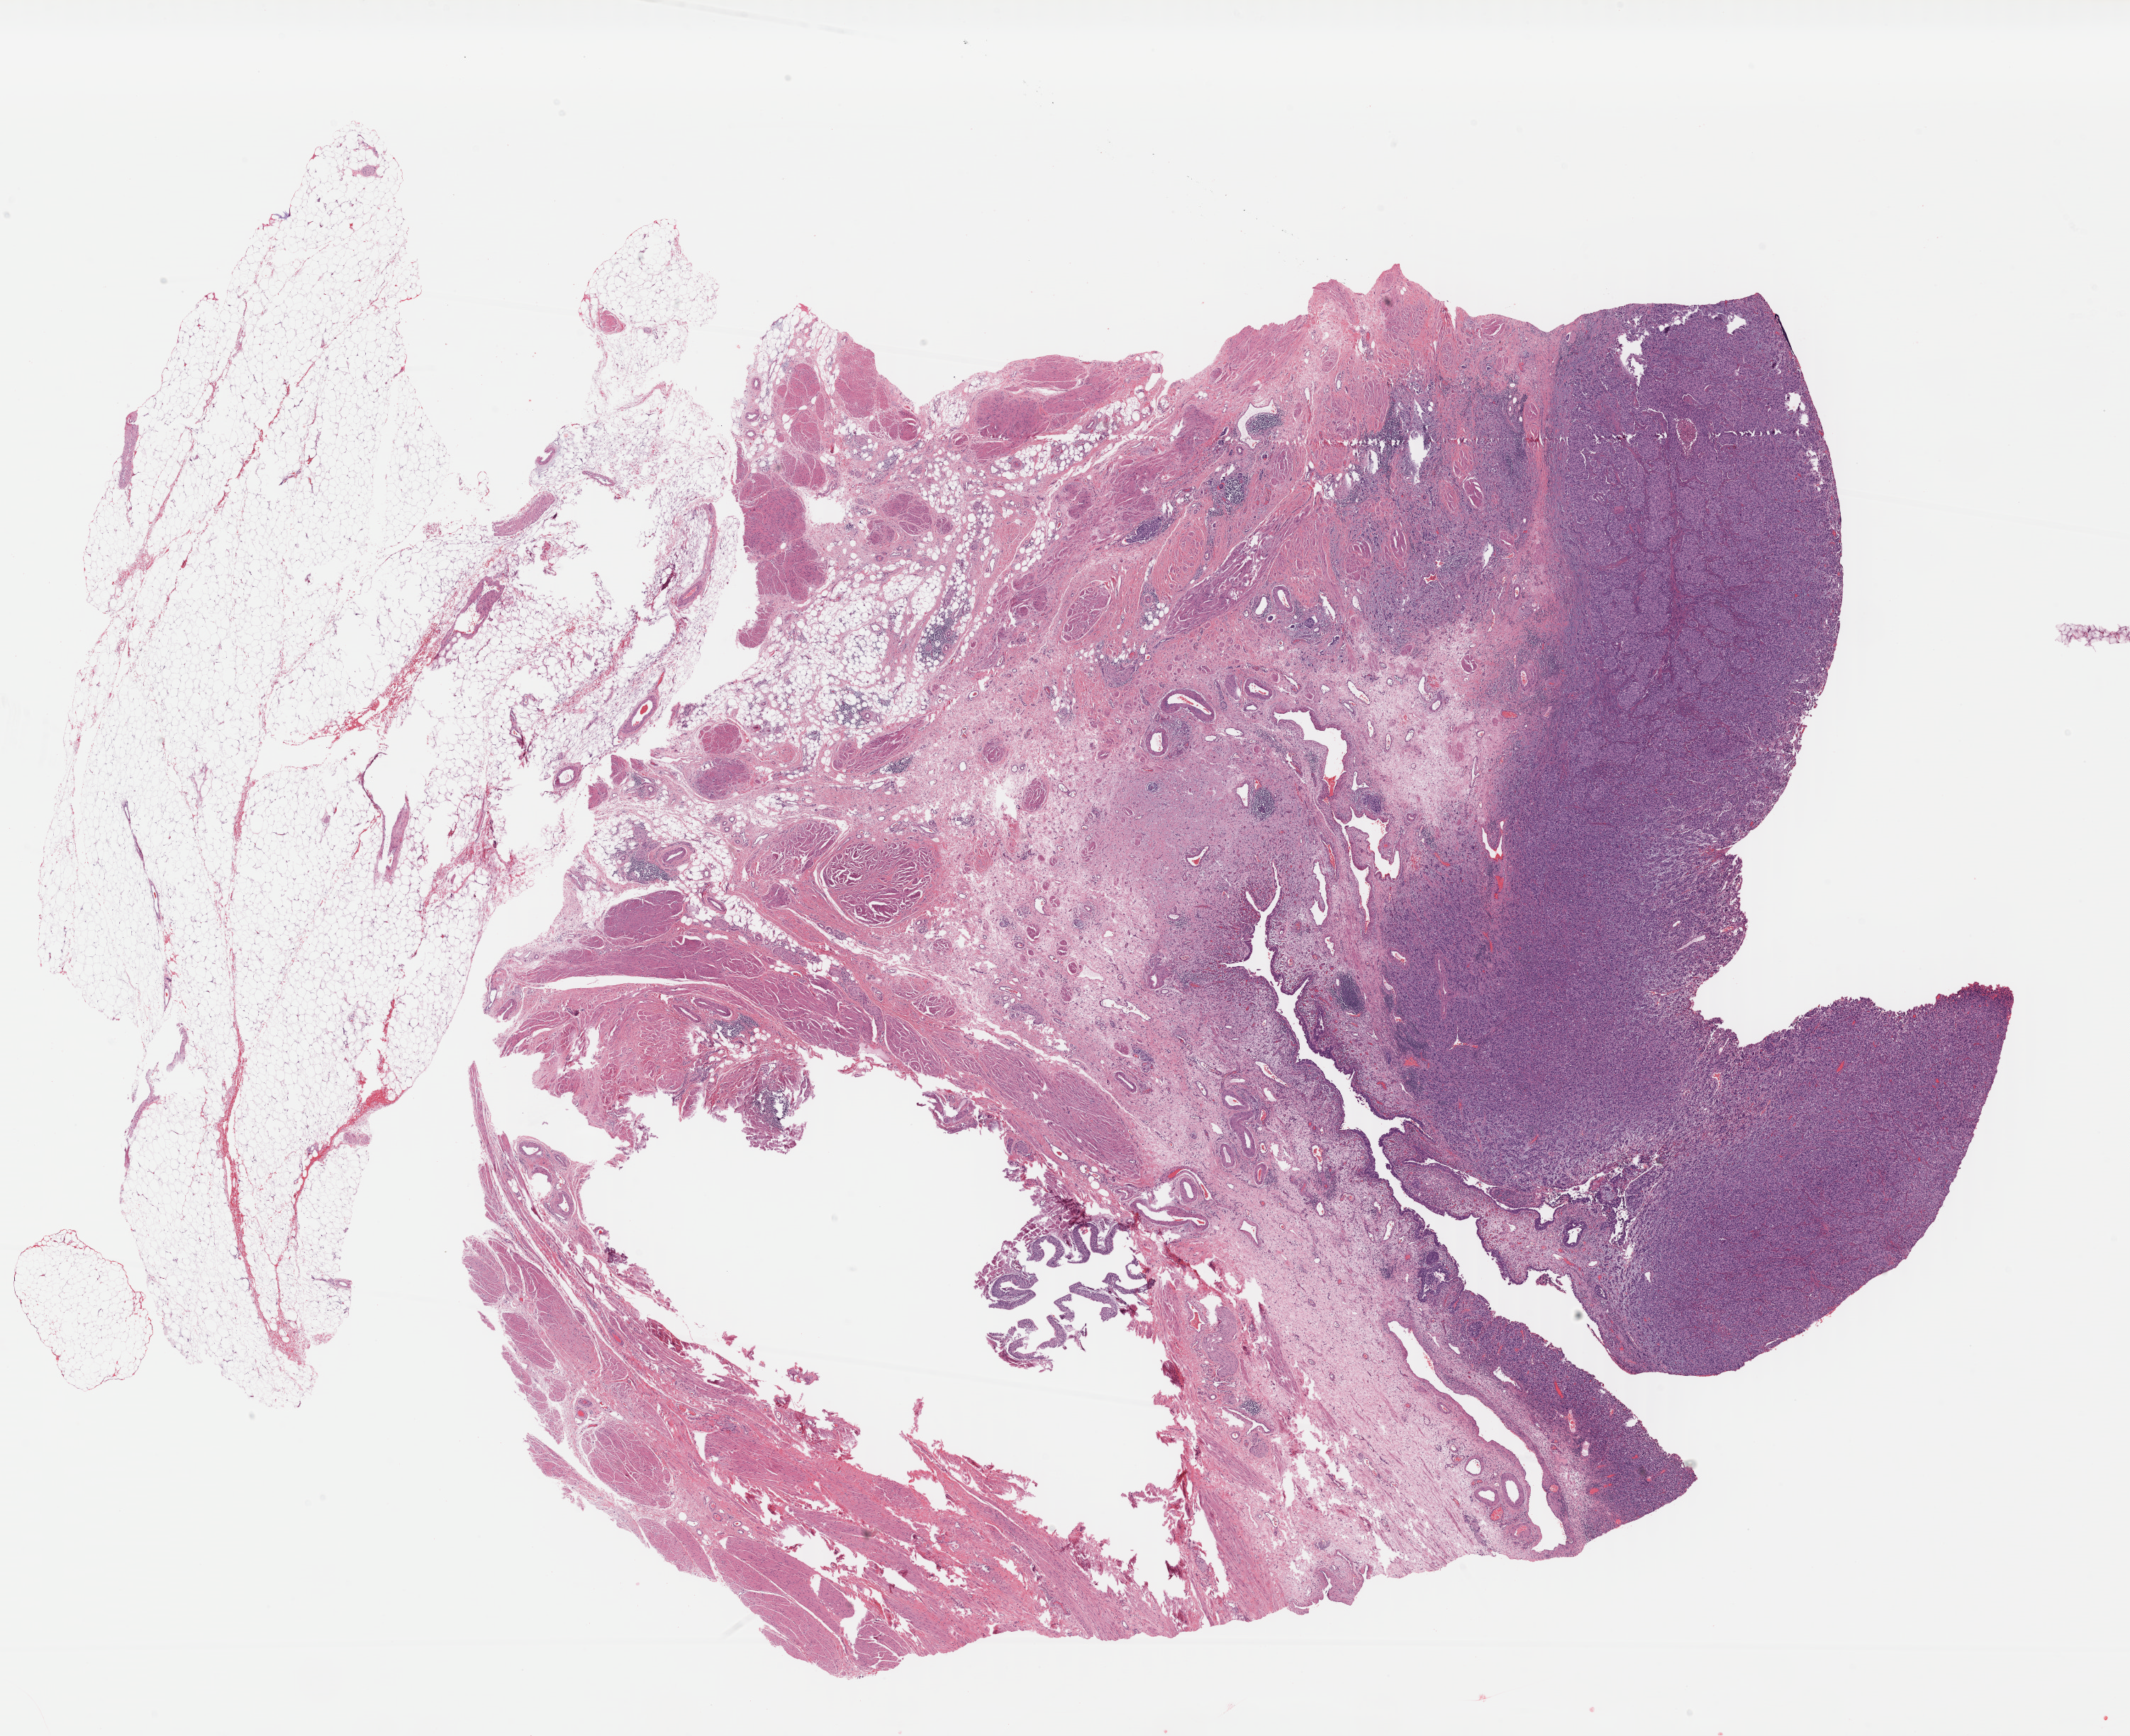
Whole-slide histology image, H&E, shown as a low-resolution overview of the whole scanned area (about 23.6 x 19.3 mm, acquisition: 40x scan); FFPE section; primary tumour sample from the bladder. Male, age 76 years at initial diagnosis.
Diagnosis: Transitional cell carcinoma.